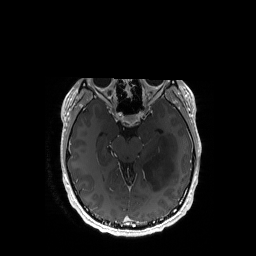
Brain MRI from a brain-tumour surgery series, one axial slice. Position 105 of 192 along the scan axis. T1-weighted post-contrast. 1 mm slice thickness. 256 × 256 image matrix. Case-level facts recorded for this patient, not image findings: histopathology: Astrocytoma; WHO grade: 3.
Structures marked on this image (expert manual segmentation):
- tumour: bounding box <142,132,177,191> (left, top, right, bottom; pixels)